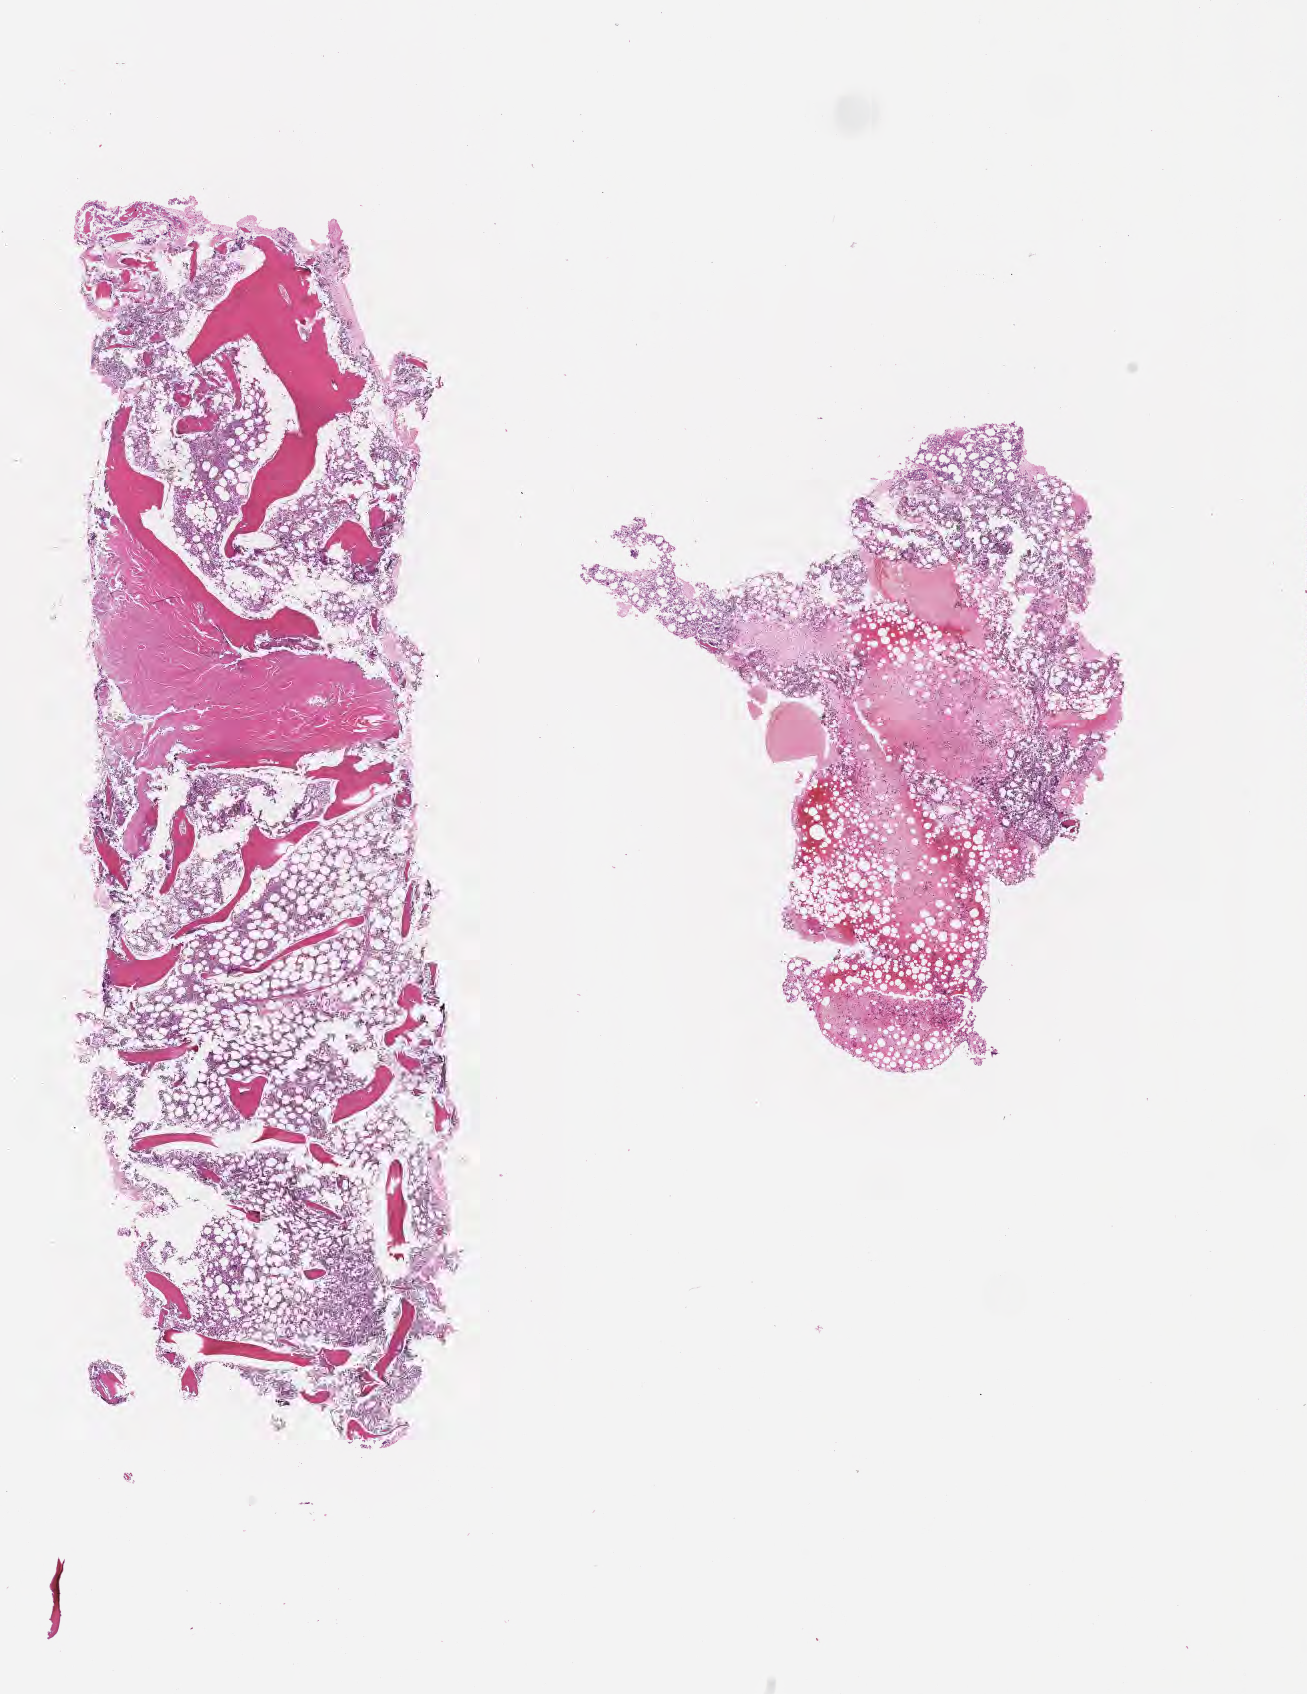
H&E whole-slide image — whole scanned area (about 10.6 x 13.7 mm) shown as a low-resolution overview. FFPE section. Non-tumor (normal tissue) sample from a patient with burkitt lymphoma, NOS. Patient: male, aged 31. Composition of this section per pathologist review: tumor cells 0%, tumor nuclei 0%, stromal cells 0%, necrosis 0%, normal cells 100%. Inflammatory infiltration, as recorded: lymphocyte infiltration 30%, monocyte infiltration 20%, neutrophil infiltration 40%.
• this section: non-tumor tissue sample; the patient's diagnosis is given above
• section: top of the tissue portion